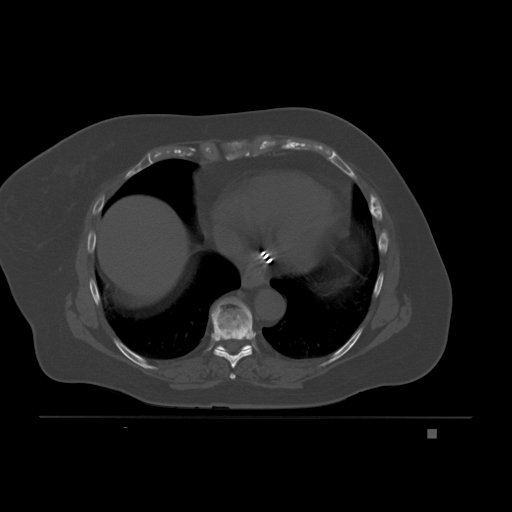
CT including the spine, one axial slice. Bone window (W 1800 / L 400 HU). 3 mm slice thickness. 512 × 512 image matrix. Patient: female, 63 years. From the clinical record (not read from this slice): primary cancer: breast.
Annotated regions visible in this slice (semi-automatic segmentation, software-assisted and operator-edited):
- T7 vertebra: box from (x=229, y=373) to (x=236, y=379) px
- T8 vertebra: (x=211, y=299)–(x=253, y=368)
- T9 vertebra: (x=212, y=307)–(x=252, y=352)